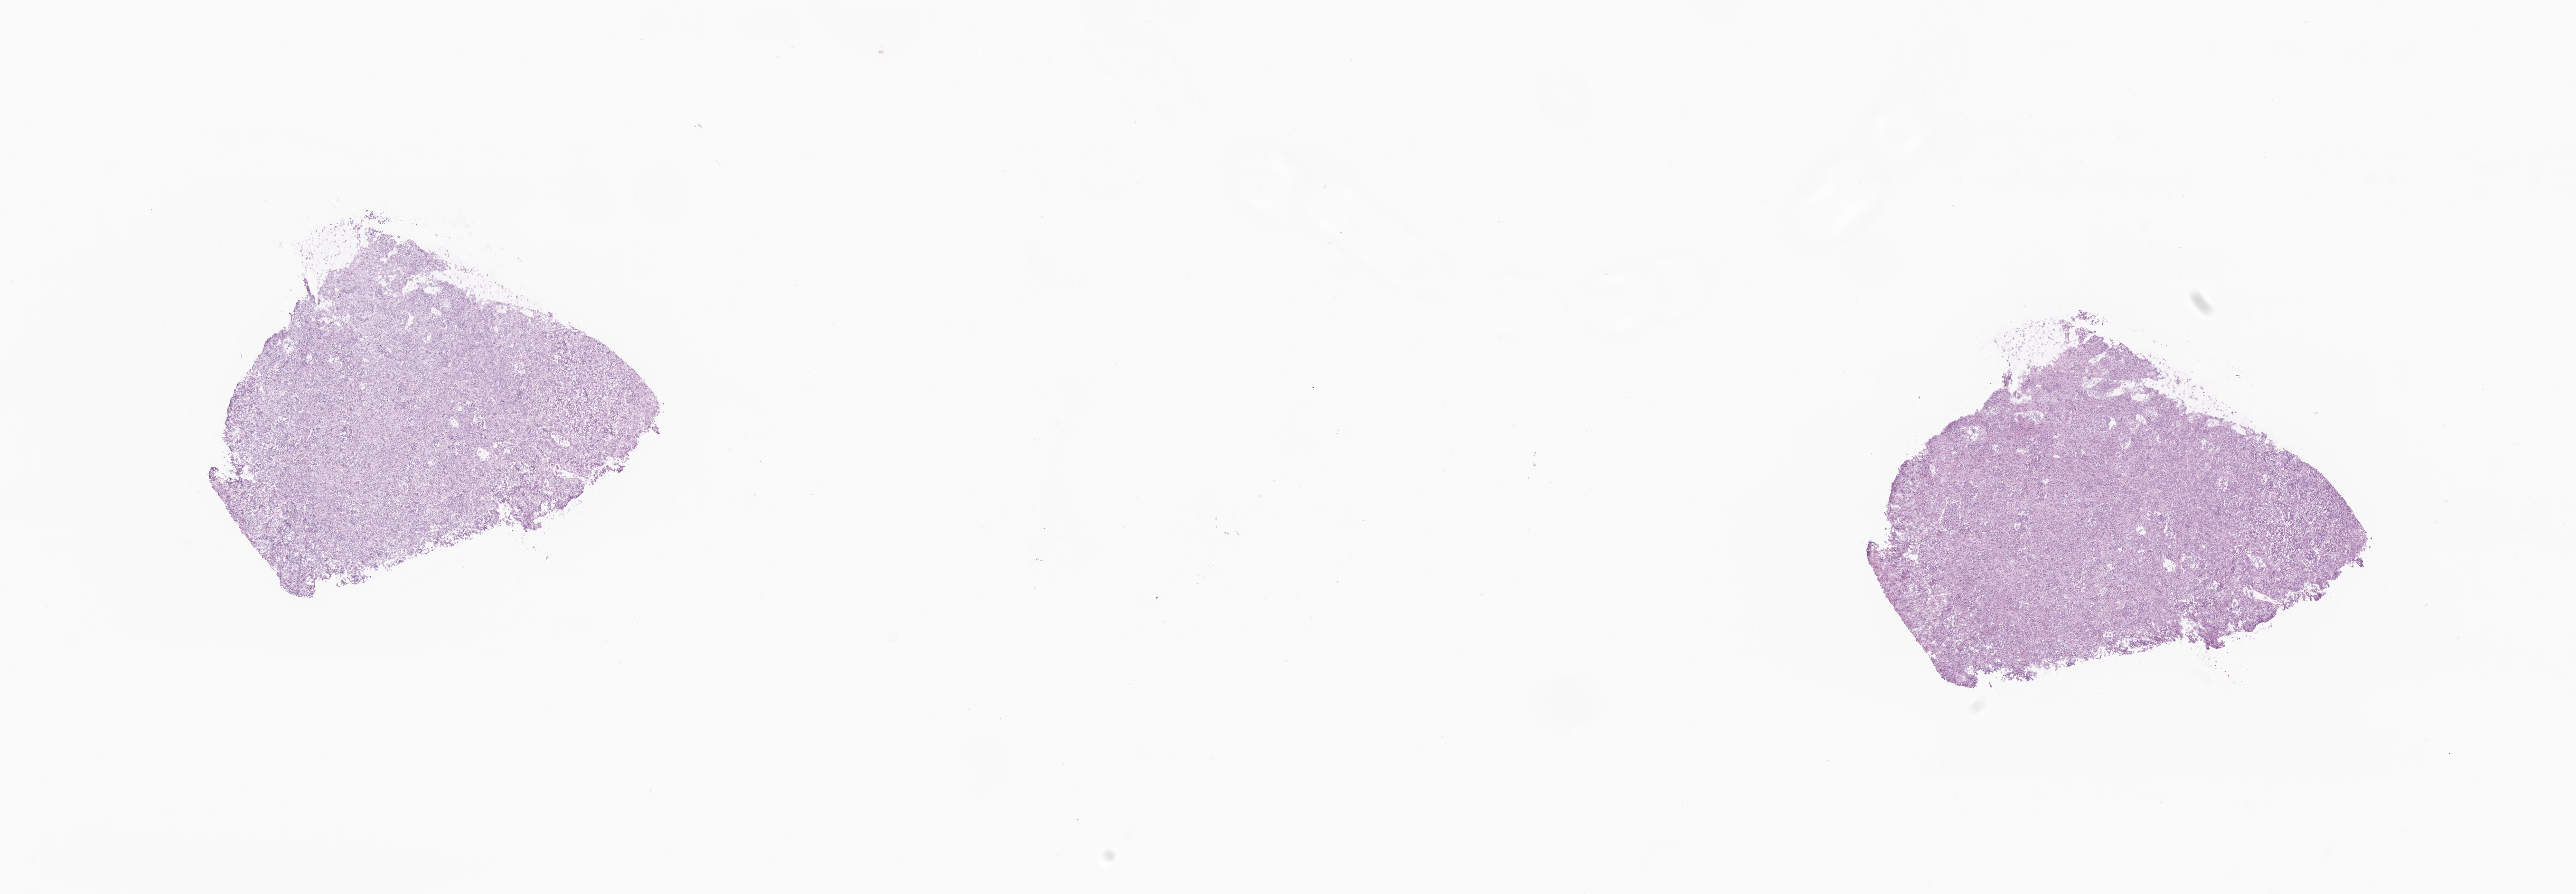
Digitized hematoxylin and eosin (H&E)-stained section — a low-resolution overview of the entire scanned area, about 22.9 x 7.9 mm, frozen section, metastatic tumor tissue, resected from adrenal gland. Female, age 65 years at initial diagnosis. Slide review estimates, as recorded: tumor cells 80%, tumor nuclei 90%.
Patient diagnosis (primary): Adenocarcinoma, NOS.